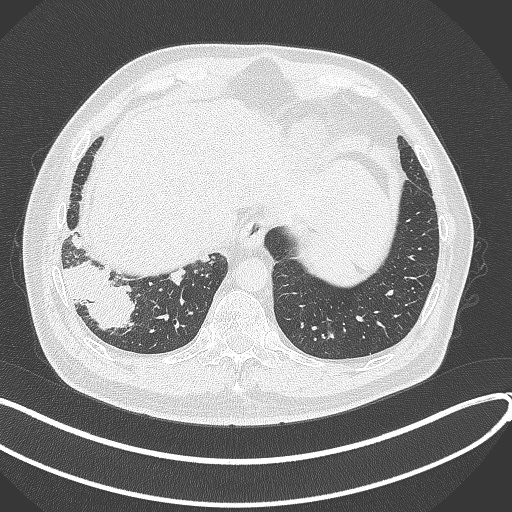
Chest CT, one axial slice. Position 66 of 360 along the scan axis. Reconstruction kernel B70f. 120 kVp. Lung window (W 1500 / L -600 HU). 1 mm slice thickness. 512 × 512 image matrix, field of view 400 × 400 mm. Male patient, age 59 years.
Structures marked on this image (bounding box drawn by a radiologist):
- lung tumour (recorded histology: adenocarcinoma): bounding box (x1, y1, x2, y2) in pixels: (60, 255, 134, 332)